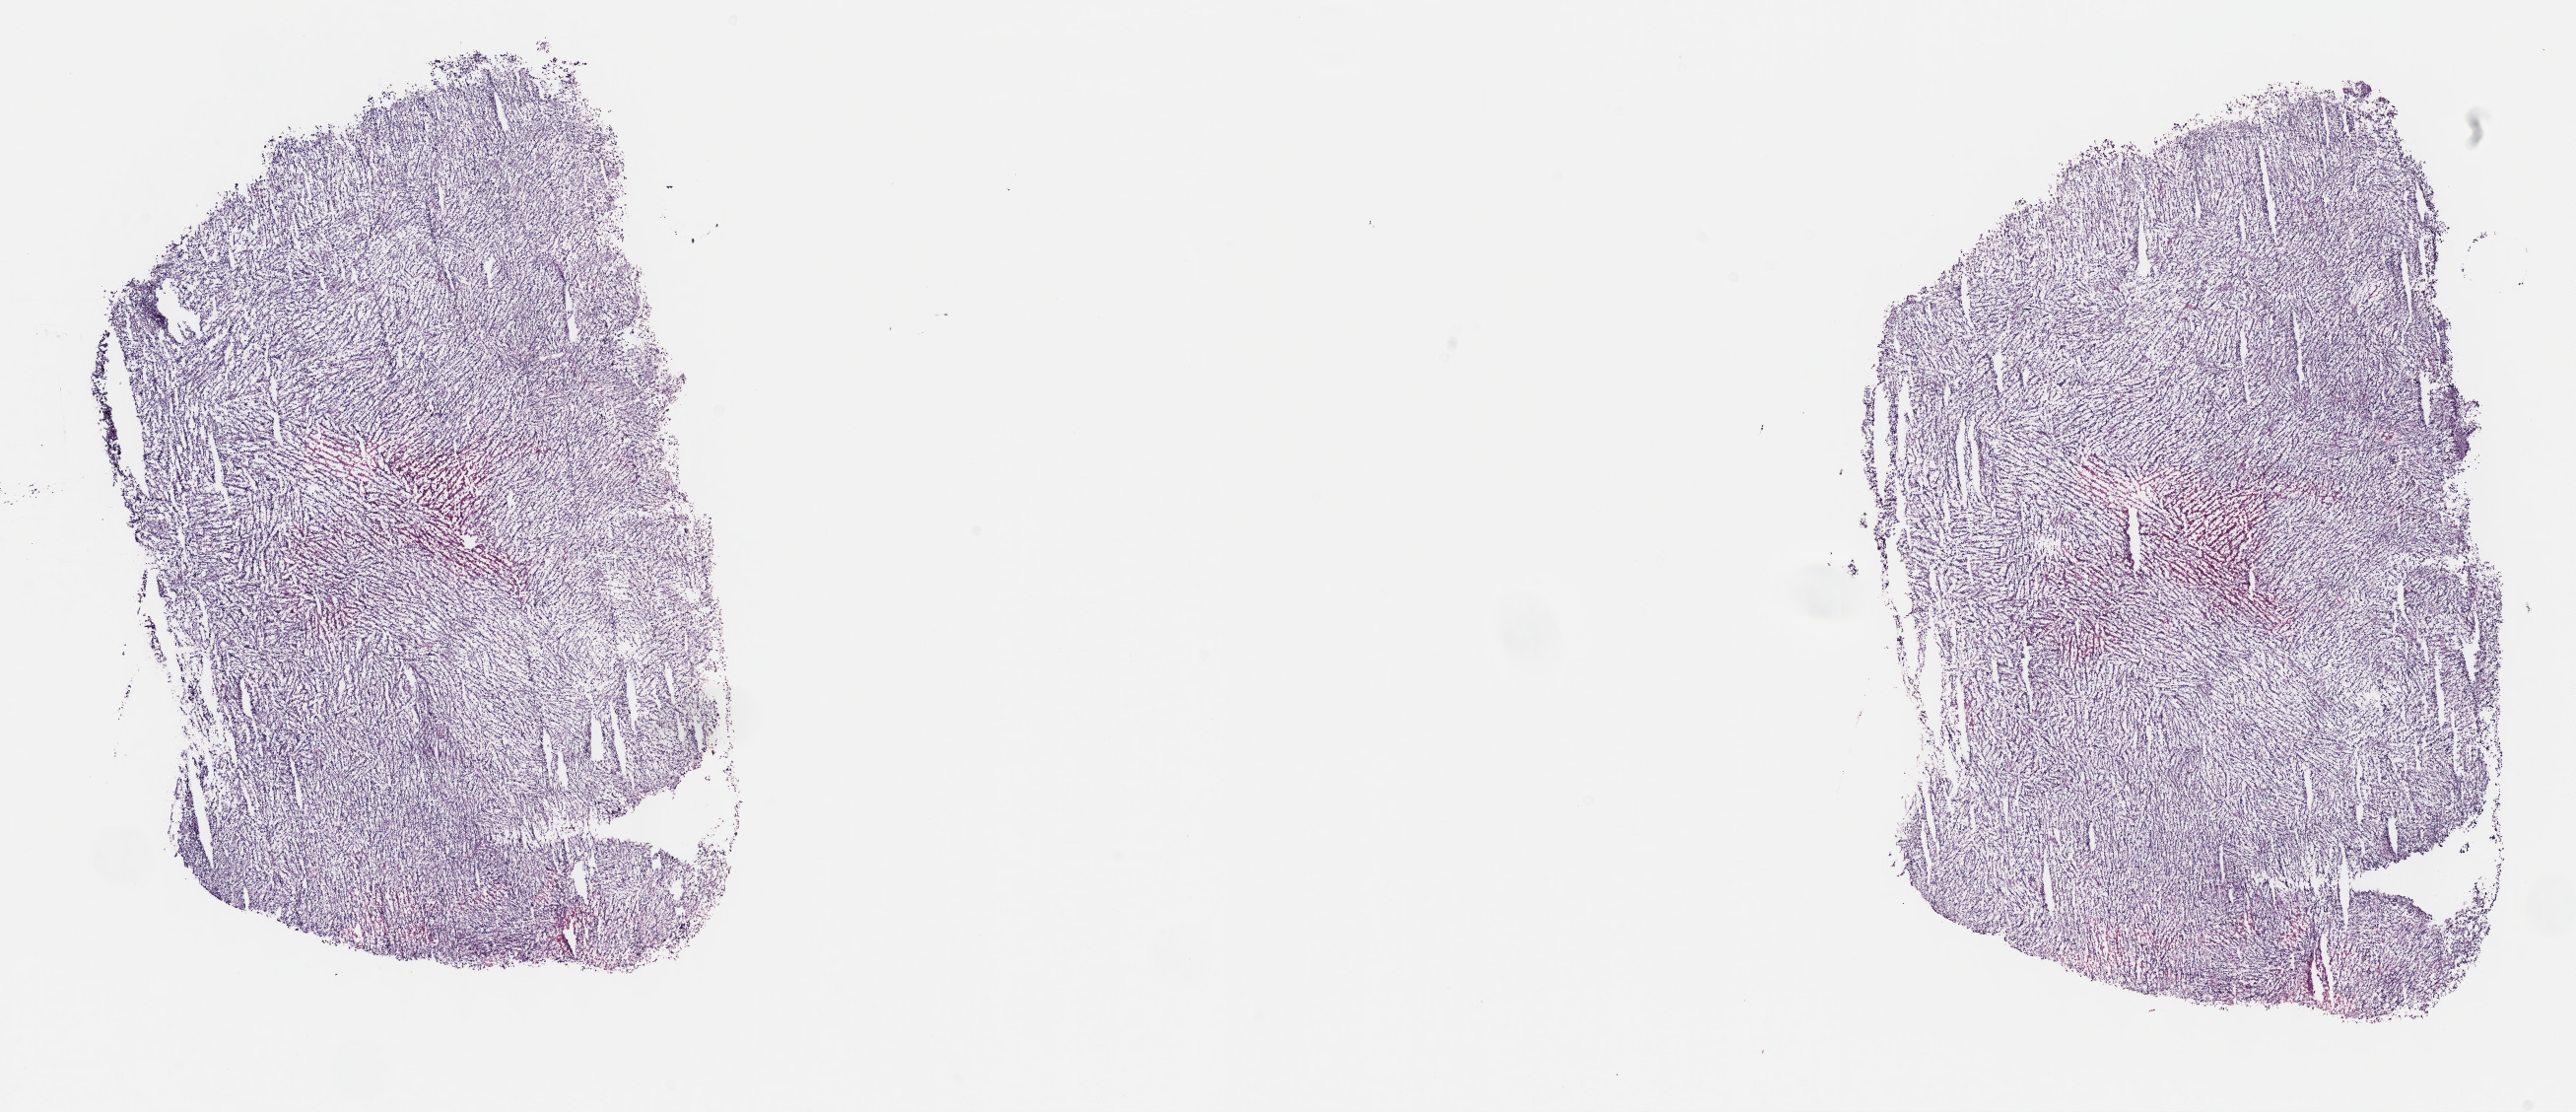
H&E whole-slide image, a low-resolution overview of the entire scanned area, about 21.1 x 9.1 mm (slide scanned at 40x), frozen section, sample: primary tumour, testis. Patient: male, age at initial diagnosis 47 years. Slide review estimates, as recorded: tumour cells 80%, tumour nuclei 80%.
Diagnosis: Seminoma, NOS.